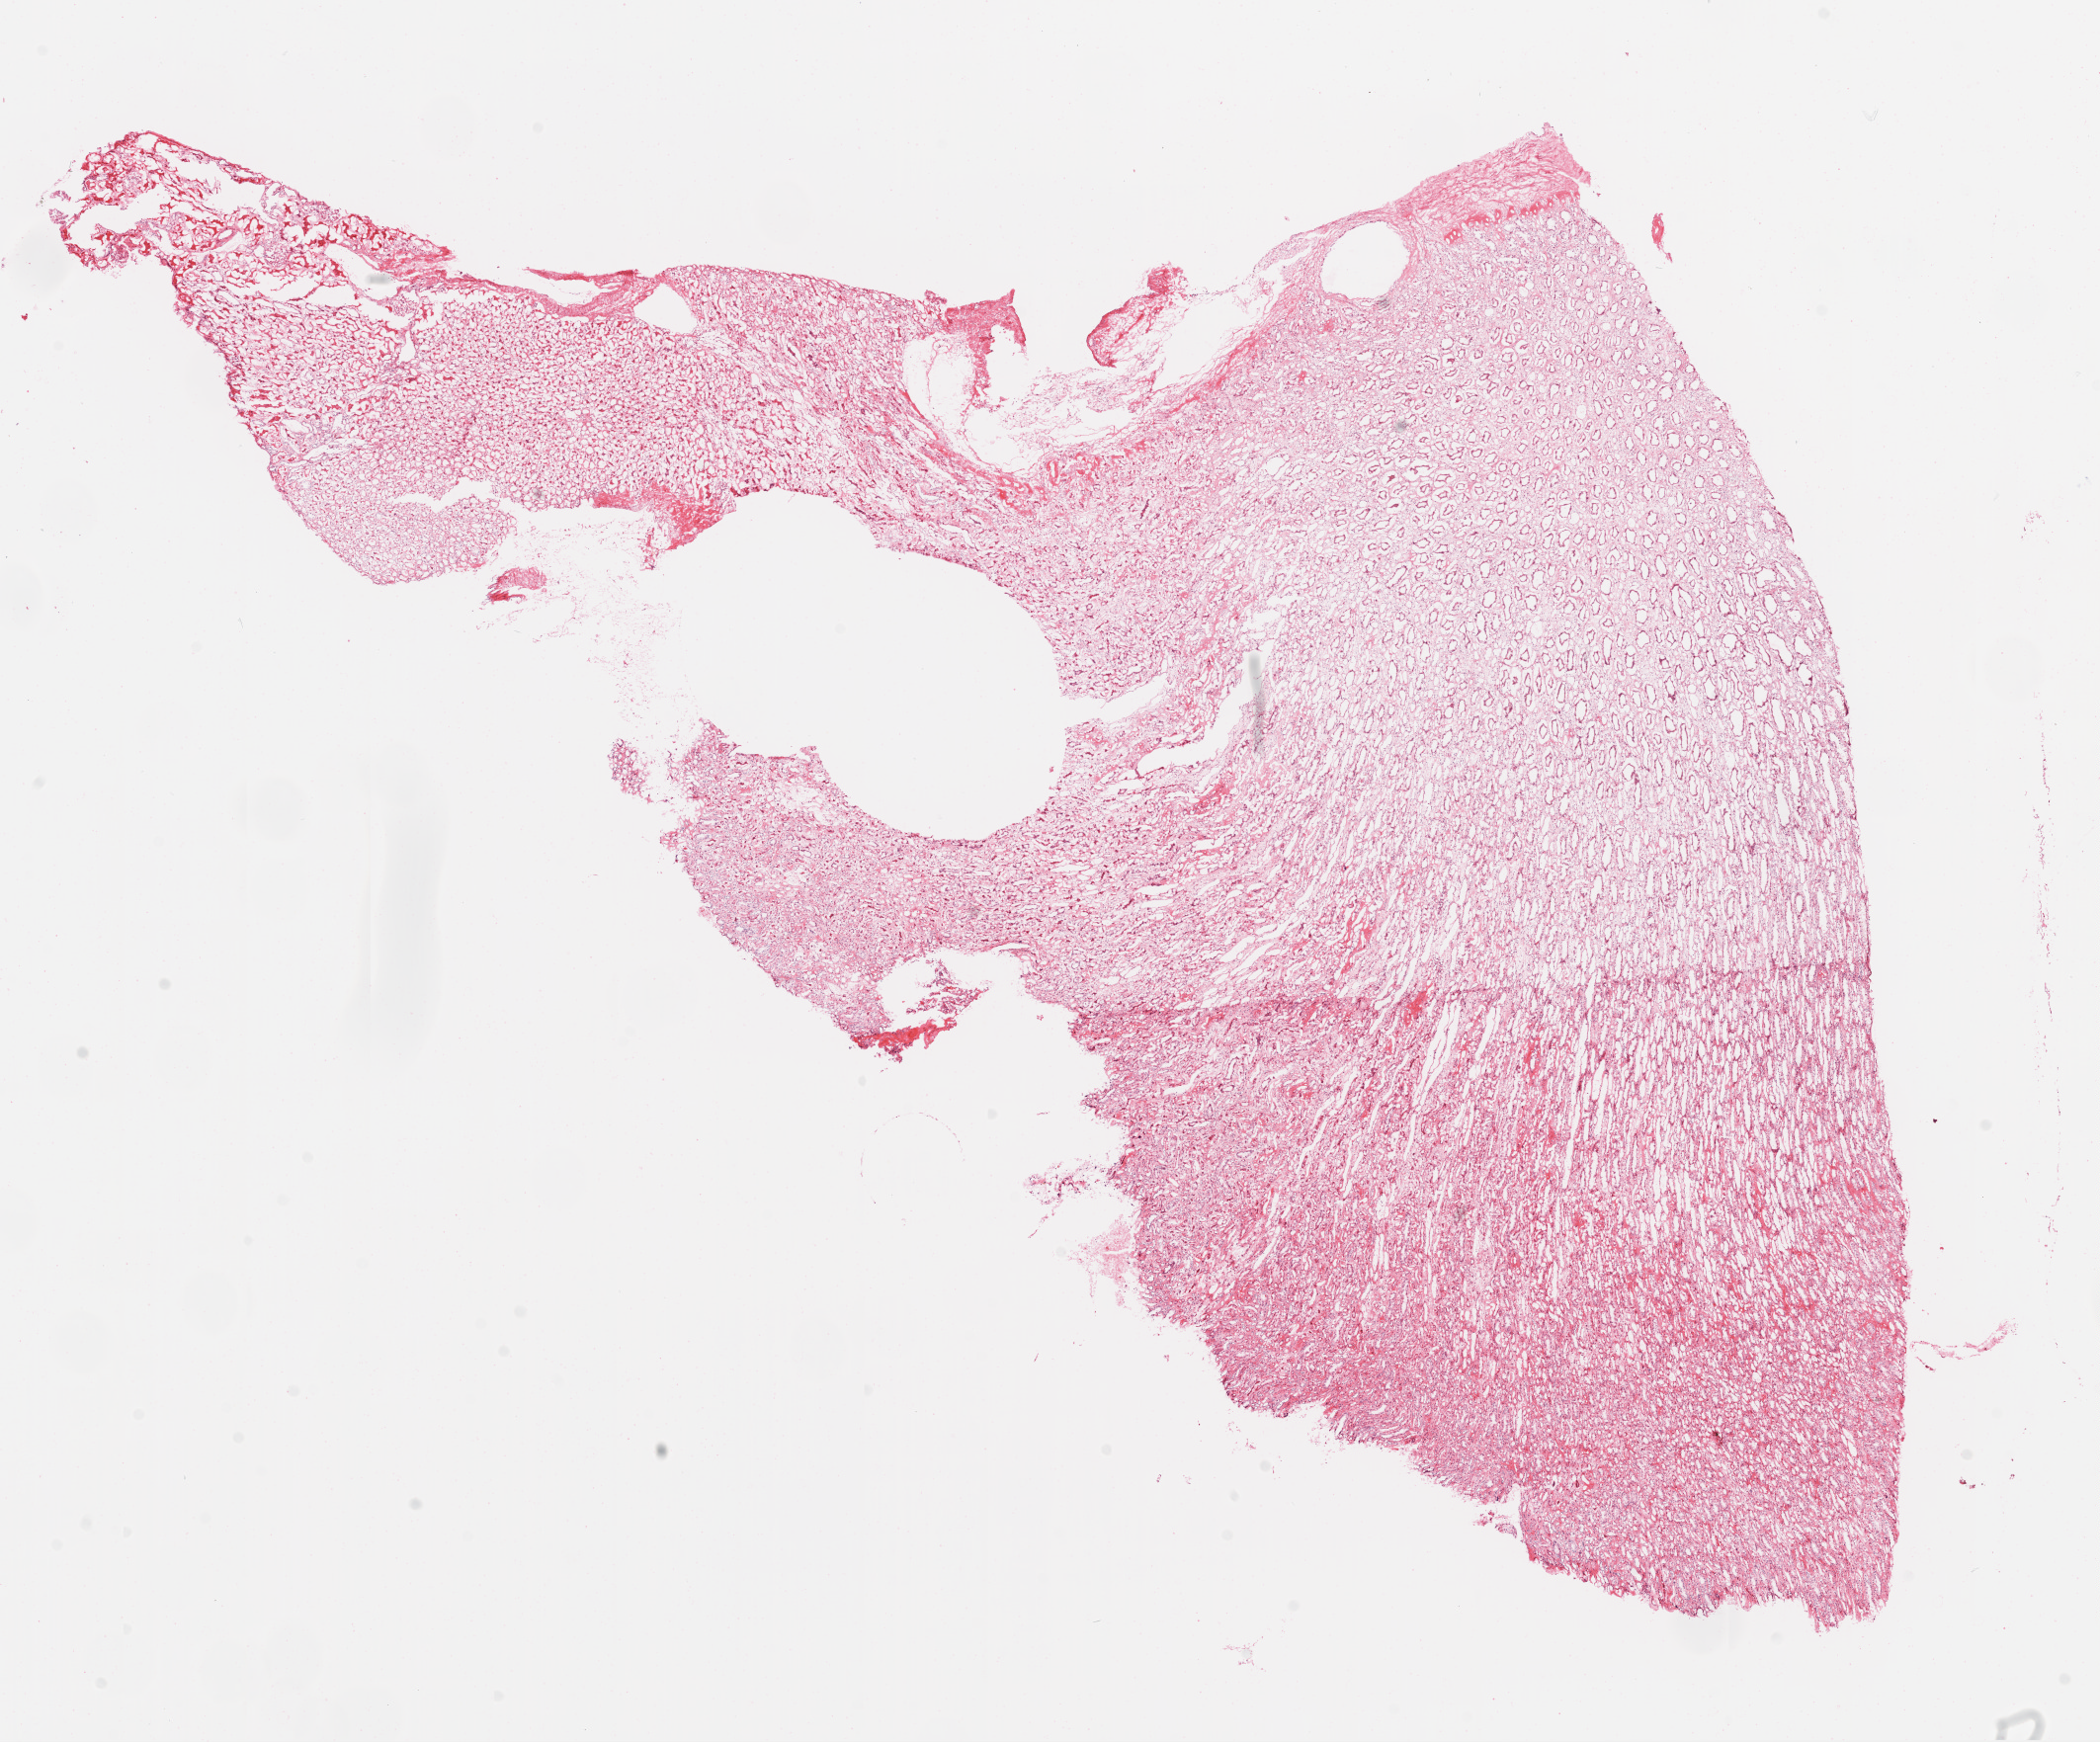
Whole-slide histology image, H&E, a low-resolution overview of the entire scanned area, about 17.1 x 14.1 mm (slide scanned at 20x). Frozen section from the top of the tissue portion. Kidney, solid tissue normal (non-tumour tissue) sample. Patient: male, age at initial diagnosis 57 years.
* this section: solid tissue normal sample (biorepository sample class)
* patient diagnosis: Clear cell adenocarcinoma, NOS